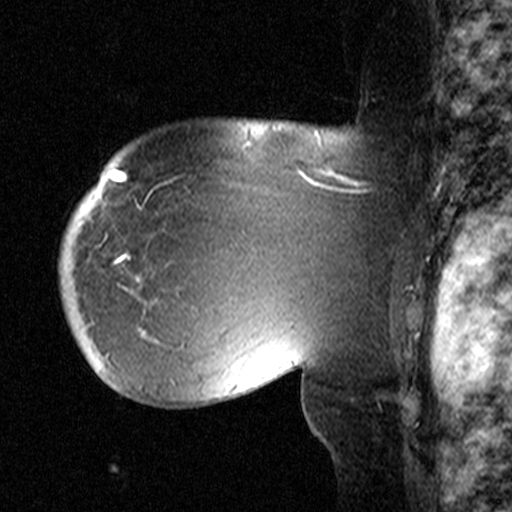
Breast MRI (dynamic contrast-enhanced), one sagittal slice. Position 34 of 44 along the scan axis. Dynamic contrast-enhanced study with each time point stored as its own series, time point 2 of 3 at this slice position (early post-contrast, ordered by acquisition time). 1.5 T. TE 4.5 ms, TR 11 ms. 3.27 mm slice thickness. 512 × 512 image matrix, field of view 200 × 200 mm. Female patient, age 53 years. From the clinical record (not read from this slice): setting: breast cancer imaged before/during neoadjuvant chemotherapy; receptor status: HR-positive, HER2-negative.
Outlined on this slice (semi-automatically segmented with operator editing):
- analysis volume of interest (the breast-tissue region the enhancement analysis was run in; not a lesion): bounding box [x1, y1, x2, y2] px = [59, 154, 311, 367]
- tumour enhancement mask (voxels above the 90 % enhancement threshold inside the analysis volume of interest): [114, 255, 128, 264]